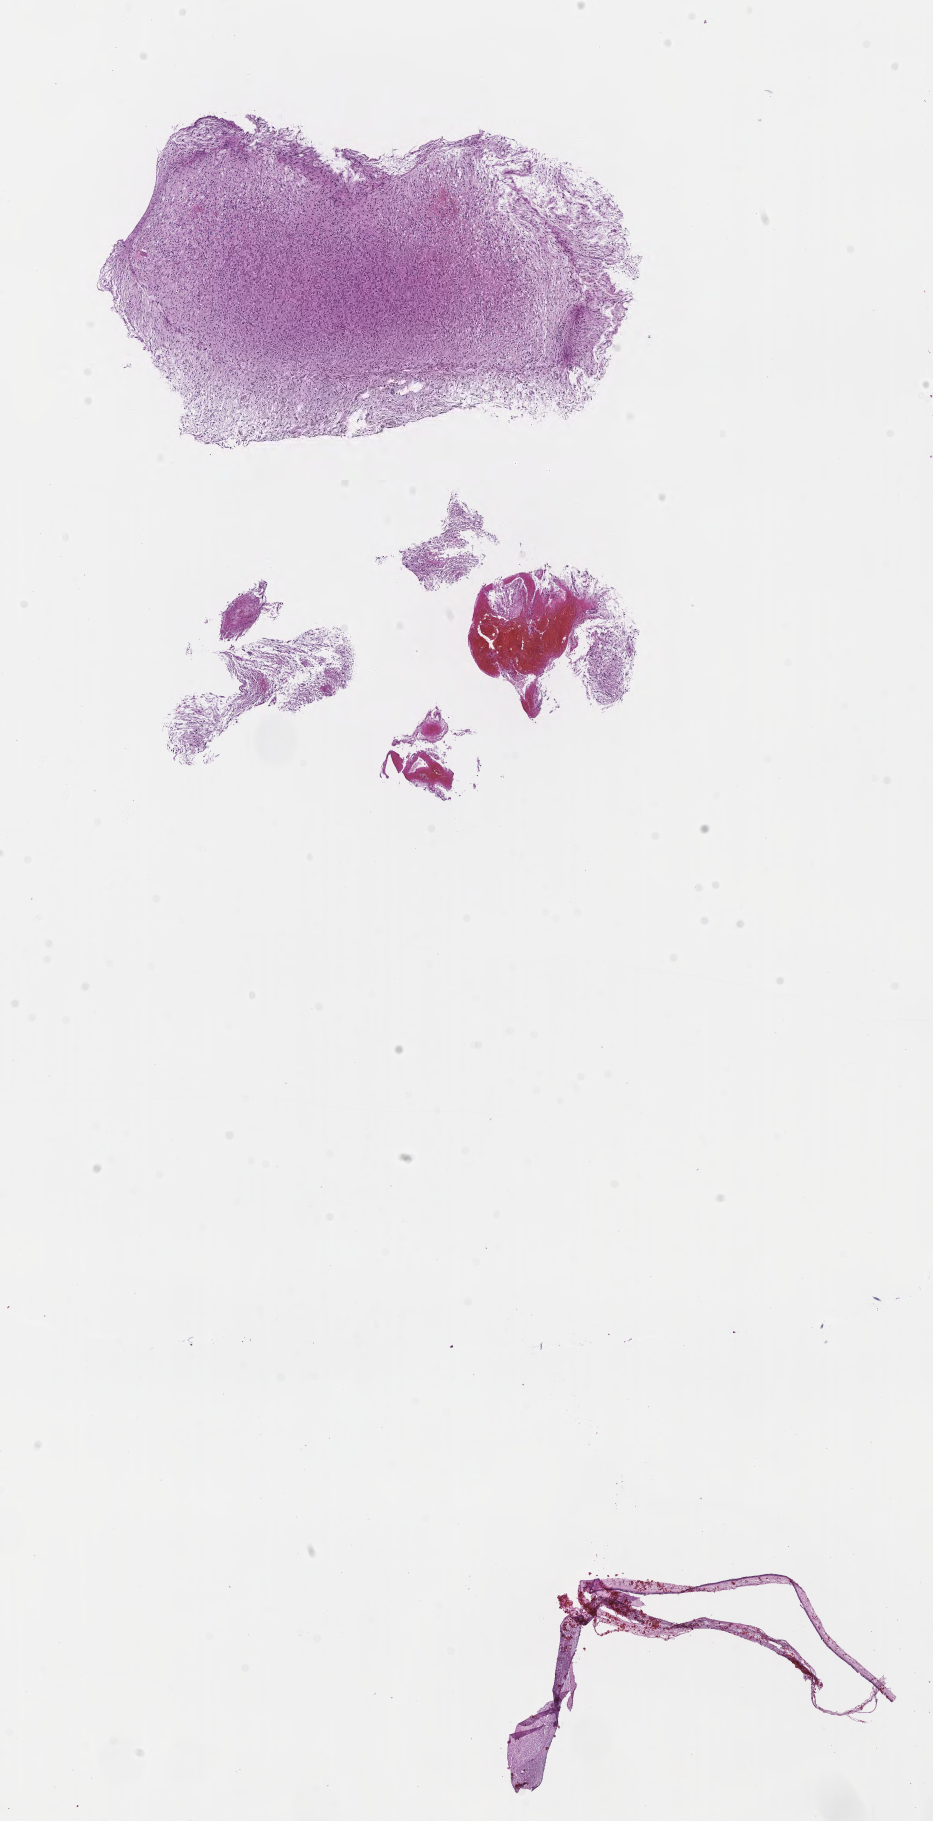
Haematoxylin and eosin whole-slide image of tumor tissue from the frontal lobe — shown as a low-resolution overview of the whole scanned area (about 7.5 x 14.7 mm). Formalin-fixed, paraffin-embedded (FFPE) tissue. Patient male; age 112 months (9 years 4 months).
- diagnosis (ICD-O-3 morphology term): Pilocytic astrocytoma